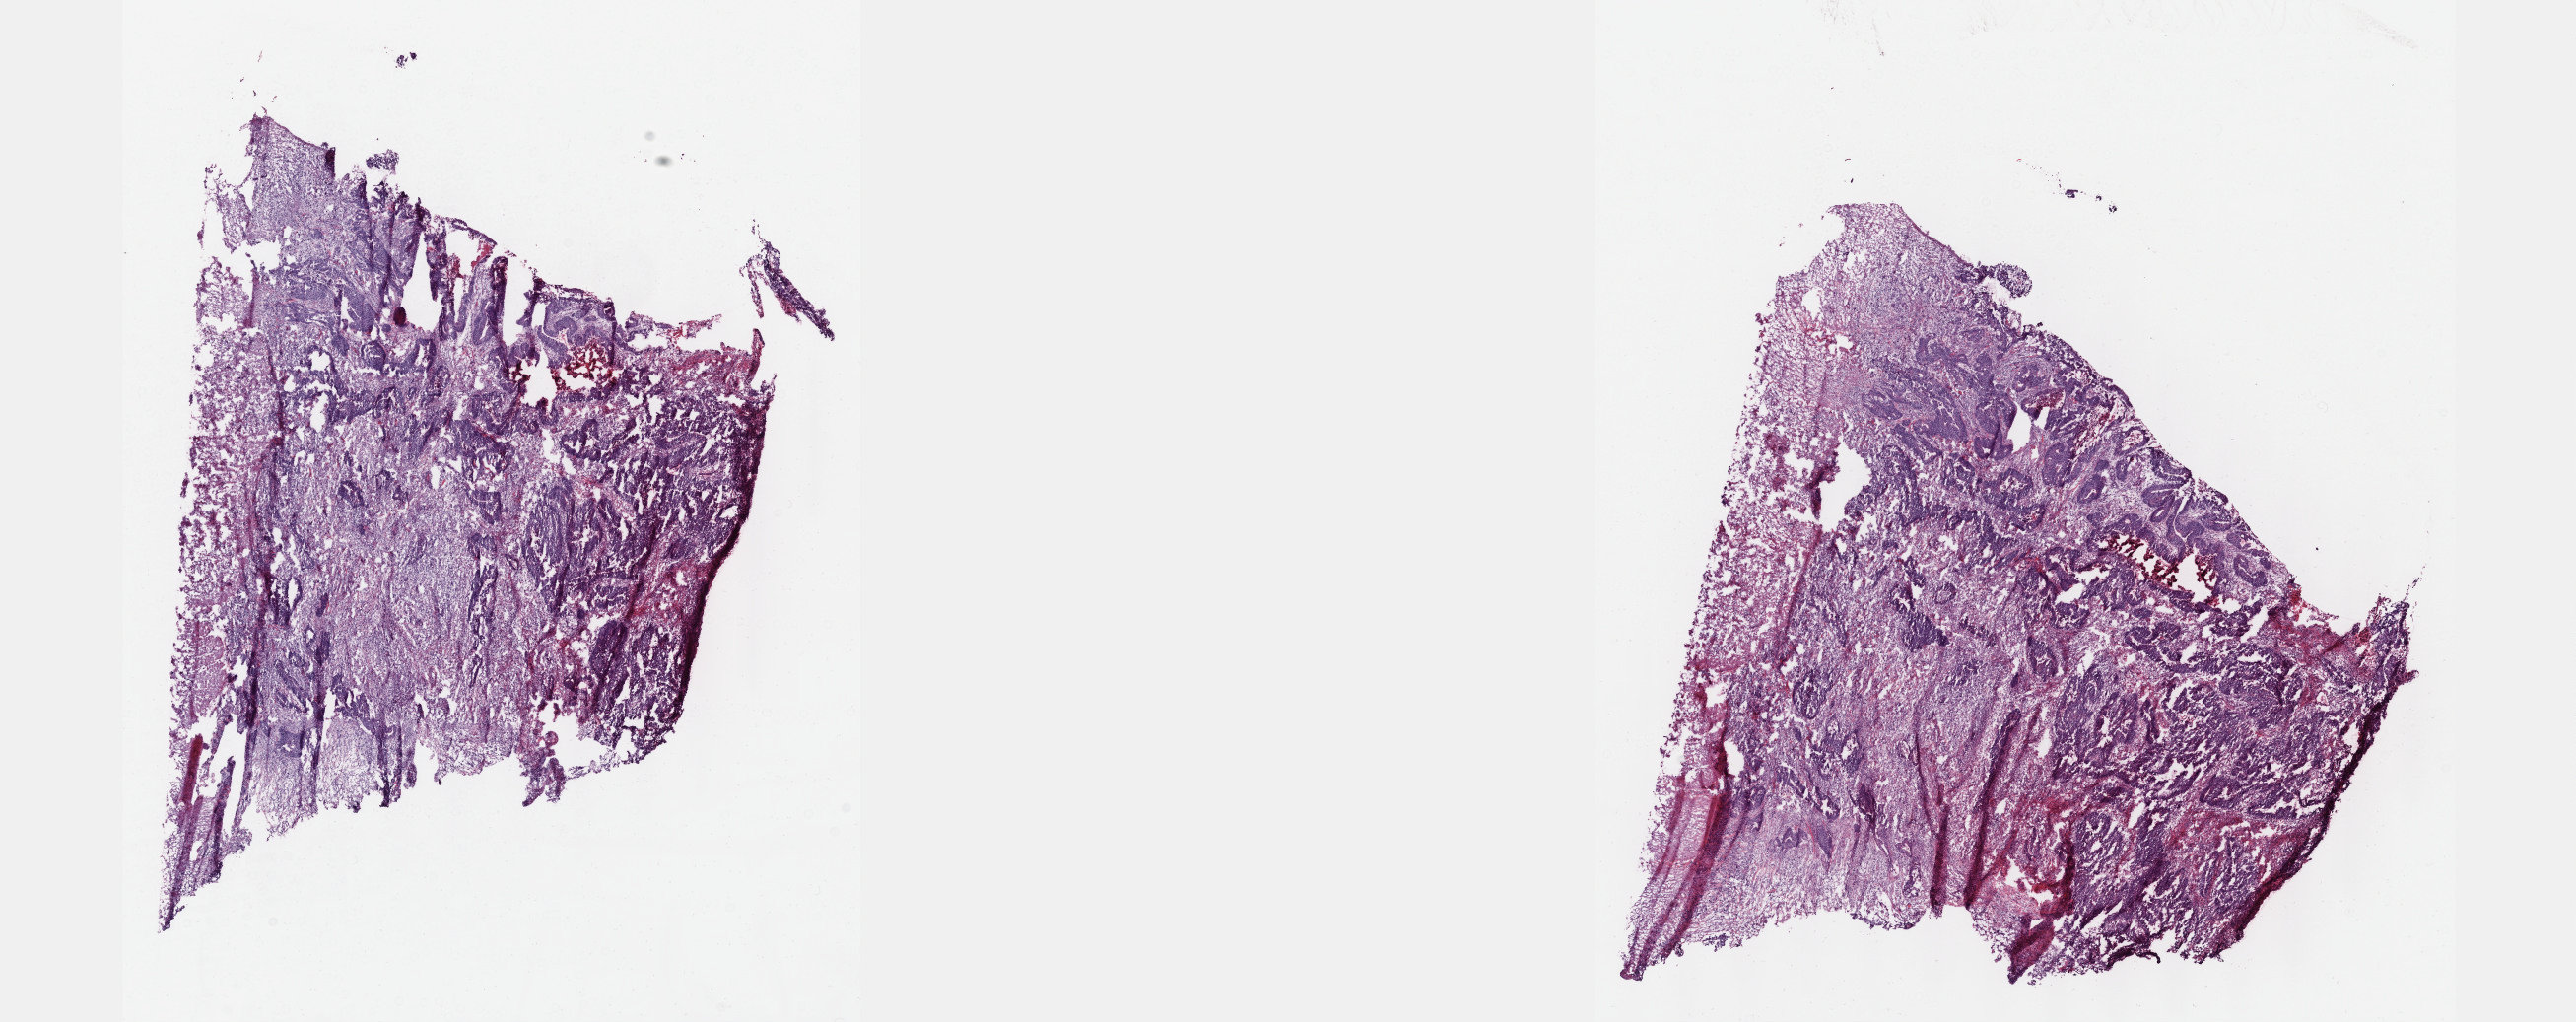
Whole-slide histology image, Hematoxylin and eosin (H&E) stained, shown as a low-resolution overview of the whole scanned area (about 21.1 x 8.4 mm, acquisition: 40x scan); frozen section; sample: primary tumour, rectum. Male patient; age at initial diagnosis 75 years.
Diagnosis: Adenocarcinoma, NOS.